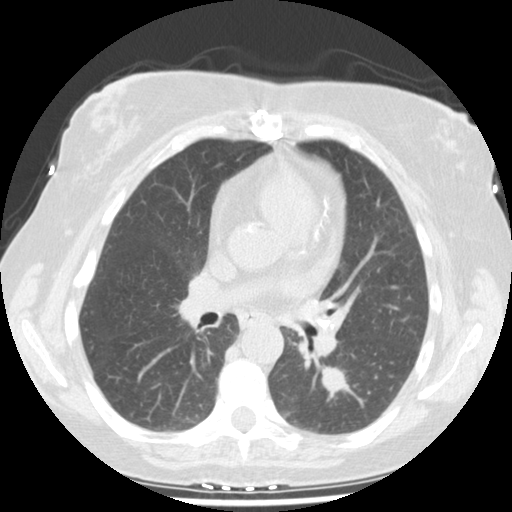
Chest CT (low-dose screening protocol), one axial image. Second screening round (one year after baseline). Lung window (W 1500 / L -600 HU). 2.5 mm slice thickness. Standard (soft-tissue) reconstruction kernel (STANDARD). 512 × 512 image matrix, field of view 326 × 326 mm. Female participant, aged 61 years at enrolment. Current smoker at enrolment.
Expert reader's lesion annotation, bounding box (x1, y1, x2, y2) in pixels: (312, 354, 365, 406). The screening reader recorded 2 non-calcified nodules or masses ≥4 mm on this exam (left lower lobe, right upper lobe); which of them this box marks is not recorded. Participant outcome: lung cancer diagnosed 69 days after this screen — squamous cell carcinoma, NOS, left lower lobe, moderately differentiated (G2), stage IA (AJCC 6th edition), 12 mm at pathology.